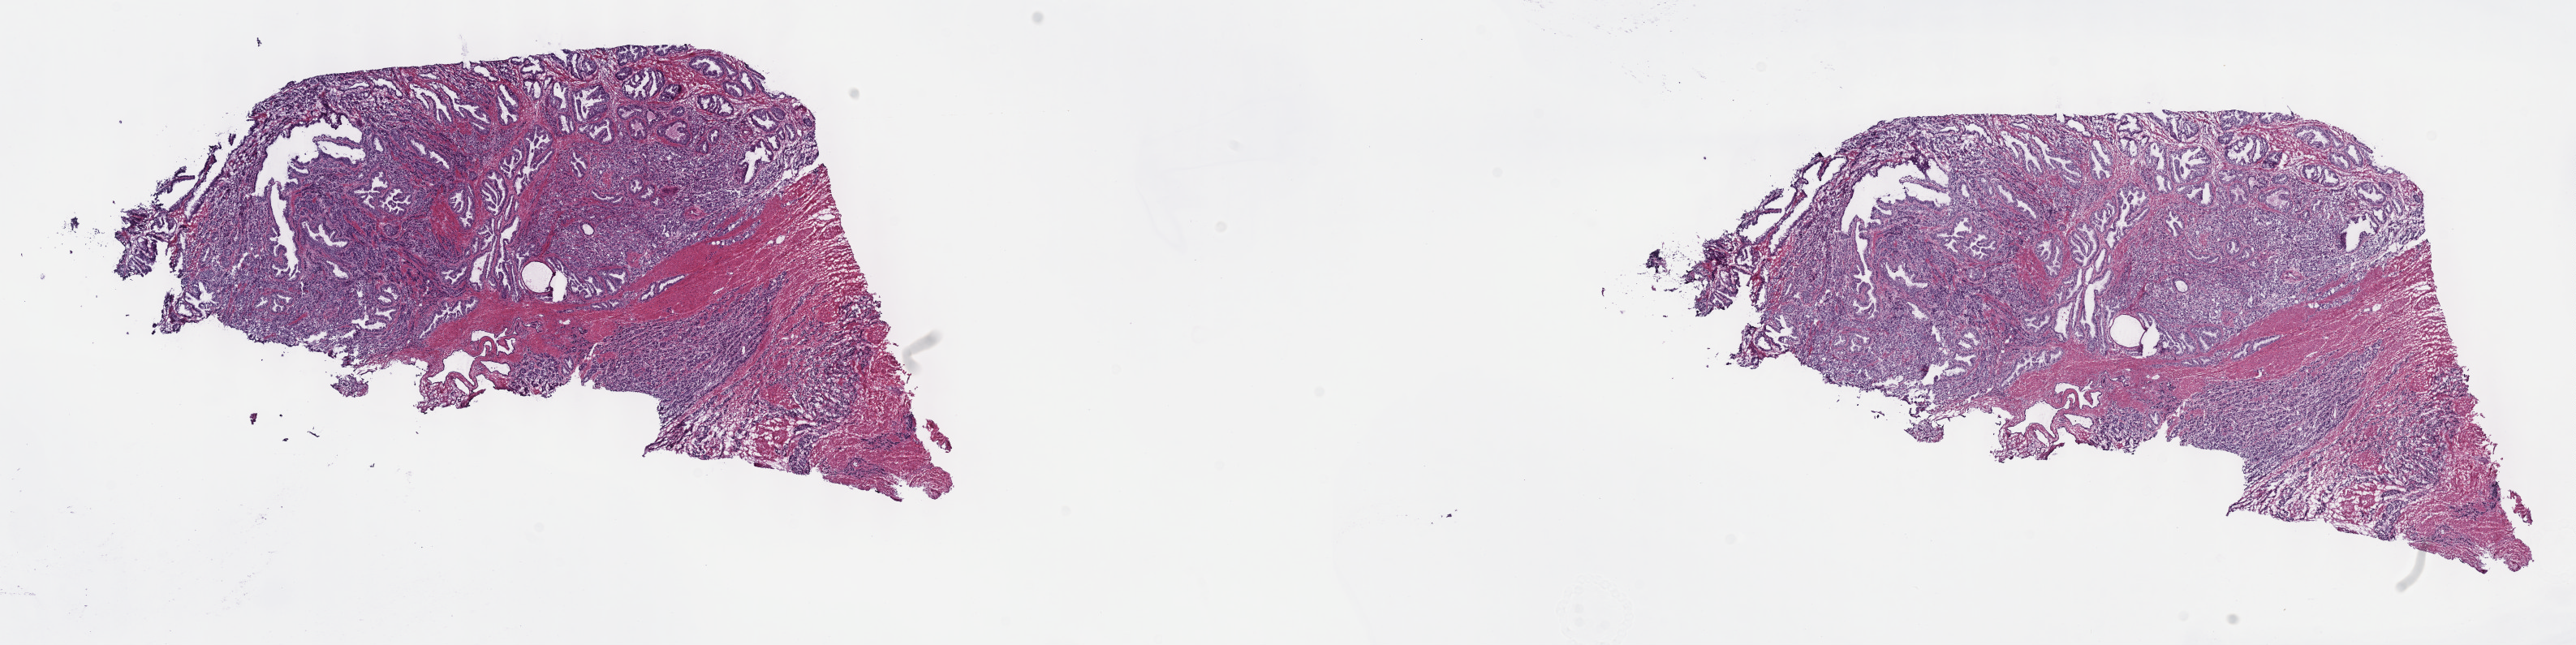
Hematoxylin and eosin (H&E) stained whole-slide image, whole scanned area (about 25.7 x 6.4 mm, acquisition: 40x scan) shown as a low-resolution overview; frozen section; sample: primary tumour, prostate. Male patient; age at initial diagnosis 62 years. Gleason score: 9 (4+5). Pathologist review of this section (percent, as recorded): tumour cells 55%, tumour nuclei 70%, normal cells 20%, stromal cells 25%, necrosis 0%. Inflammatory infiltration, as recorded: lymphocyte infiltration 0%, monocyte infiltration 0%, neutrophil infiltration 0%.
• diagnosis: Adenocarcinoma, NOS (prostate gland)
• lymph nodes positive (case pathology): 0 of 3 examined